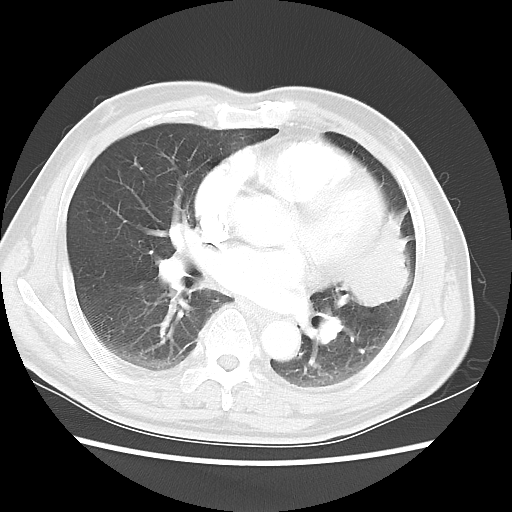
Chest CT, one axial slice. Position 23 of 50 along the scan axis. Lung window (W 1500 / L -600 HU). 512 × 512 image matrix. Patient: male, 69 years. Case-level facts recorded for this patient, not image findings: clinical TNM (as recorded): T3 N1 M1a.
Outlined on this slice (rectangle marked by the reading radiologist):
- lung tumour (recorded histology: squamous cell carcinoma): bounding box <339,200,415,315> (left, top, right, bottom; pixels)